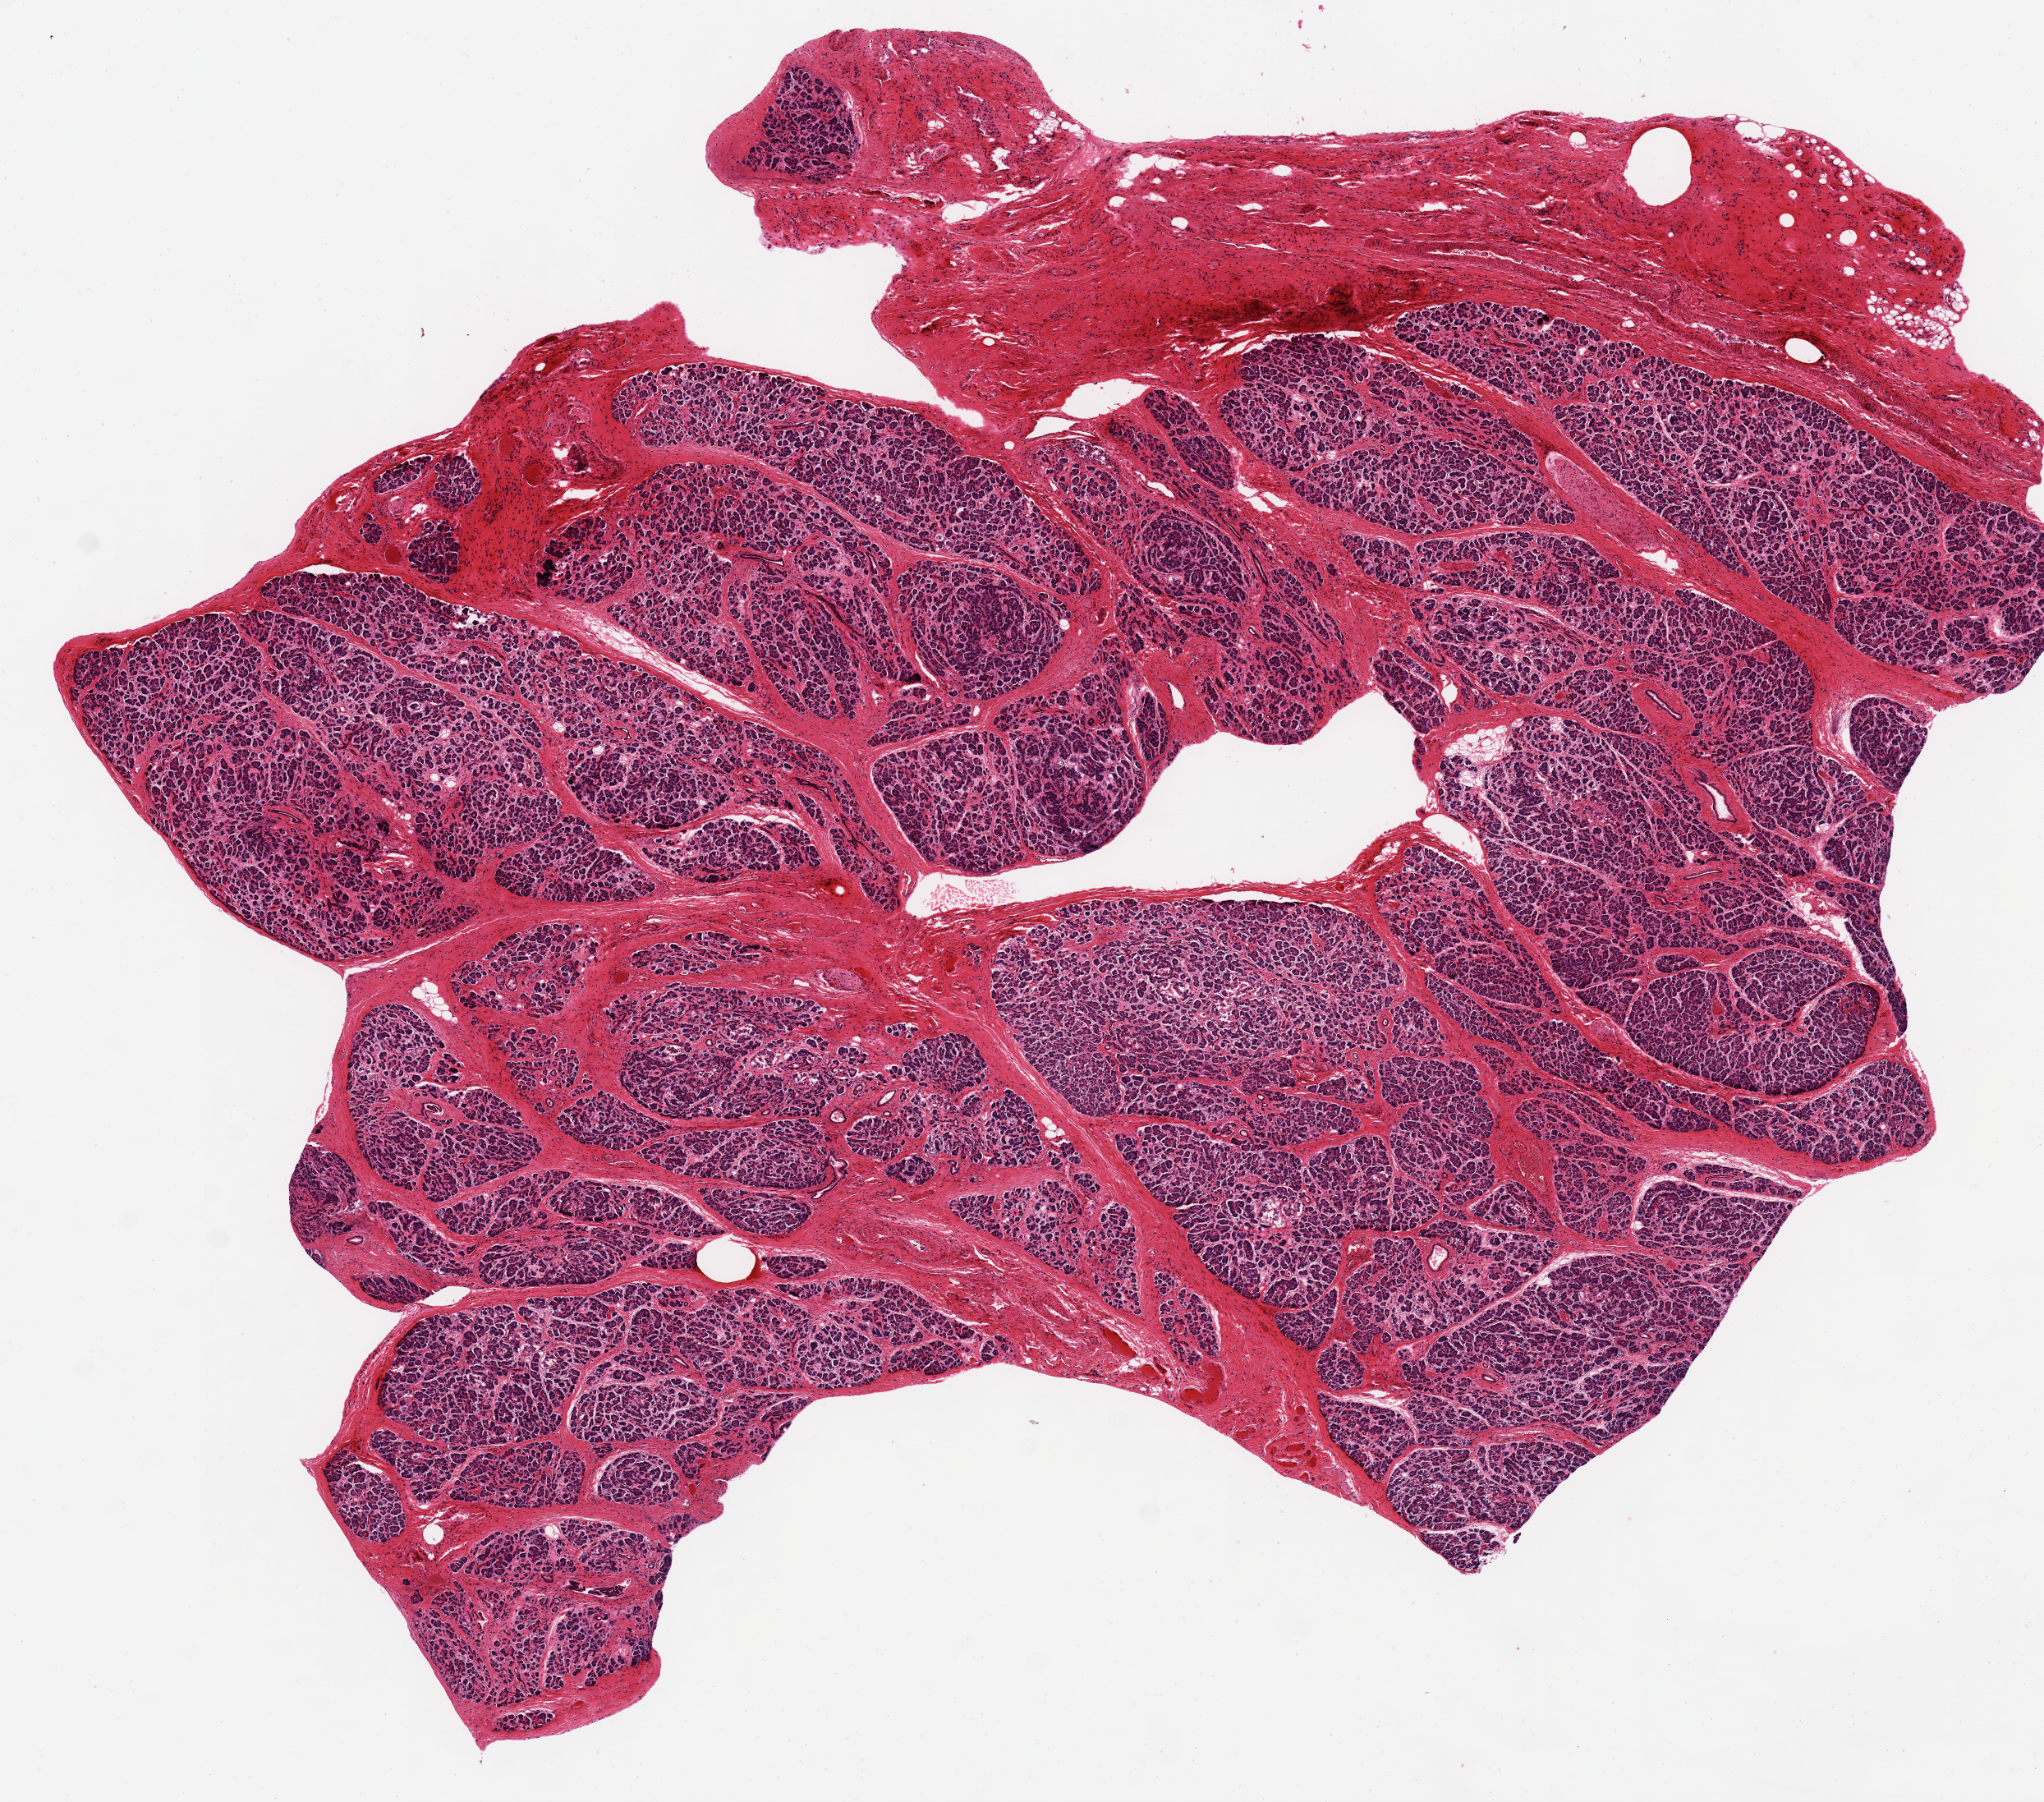
Haematoxylin and eosin whole-slide image, whole scanned area (about 9.8 x 8.7 mm, acquisition: 20x scan) shown as a low-resolution overview; PAXgene-fixed, paraffin-embedded tissue; sampled site (target tissue): pancreas; tissue donor sample. Donor: male.
• review note (as recorded): 8.7x 5.4mm. No fat, prominent fibrosis